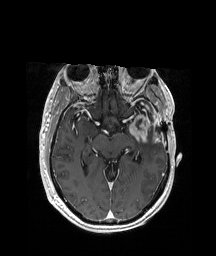
Brain MRI from a brain-tumour surgery series, one axial slice; slice 119 of 208 in the series (ordered by position); T1-weighted post-contrast; 1 mm slice thickness; 216 × 256 image matrix, field of view 228 × 270 mm. From the clinical record (not read from this slice): histopathology: Glioblastoma; WHO grade: 4; IDH mutation: no; tumour location: Left Anterior/Superior Temporal.
Annotated regions visible in this slice (outlined manually by an expert reader):
- previous resection cavity: bounding box <136,119,141,127> (left, top, right, bottom; pixels)
- tumour: <123,112,158,140>